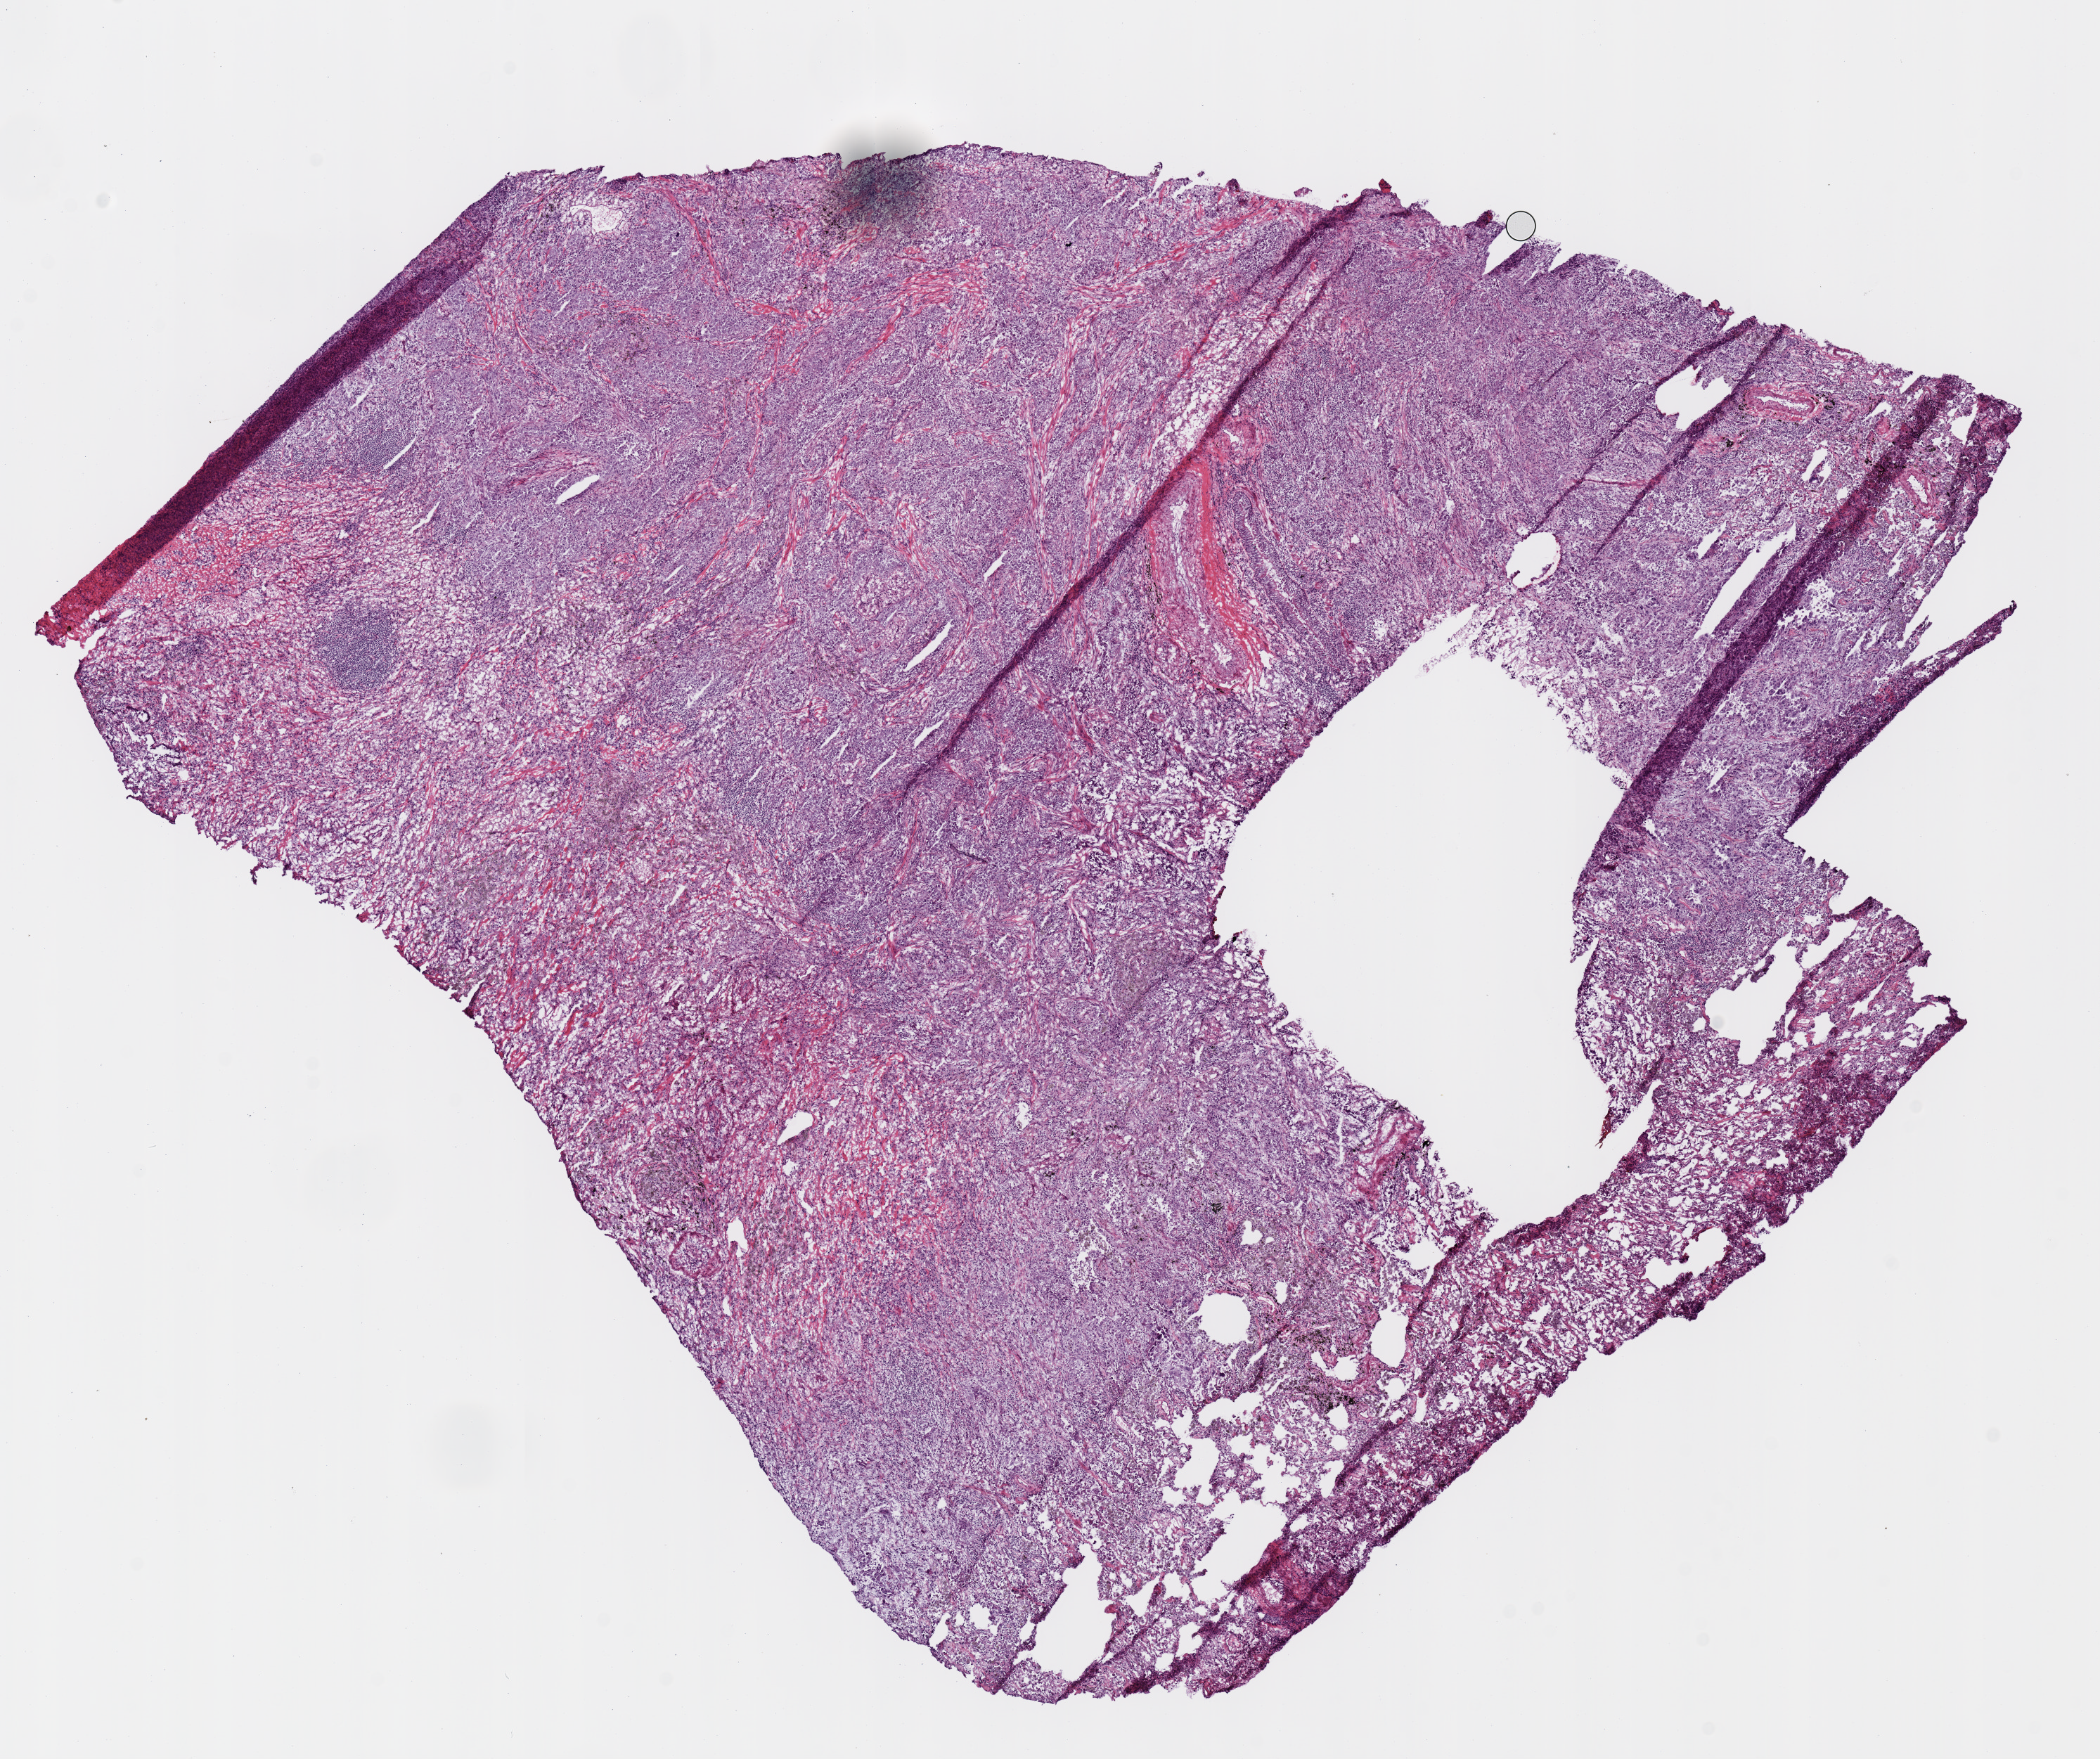
Whole-slide histology image, H&E-stained — low-resolution overview of the scanned area, about 11.8 x 9.9 mm (acquisition: 20x scan). Frozen section. Primary tumour sample from the lung. Female, age 55 years at initial diagnosis. Pathologist review of this section (percent, as recorded): tumour nuclei 75%, necrosis 0%.
AJCC pathologic stage: IB (7th edition). Histologic diagnosis: Adenocarcinoma, NOS (lower lobe, lung).